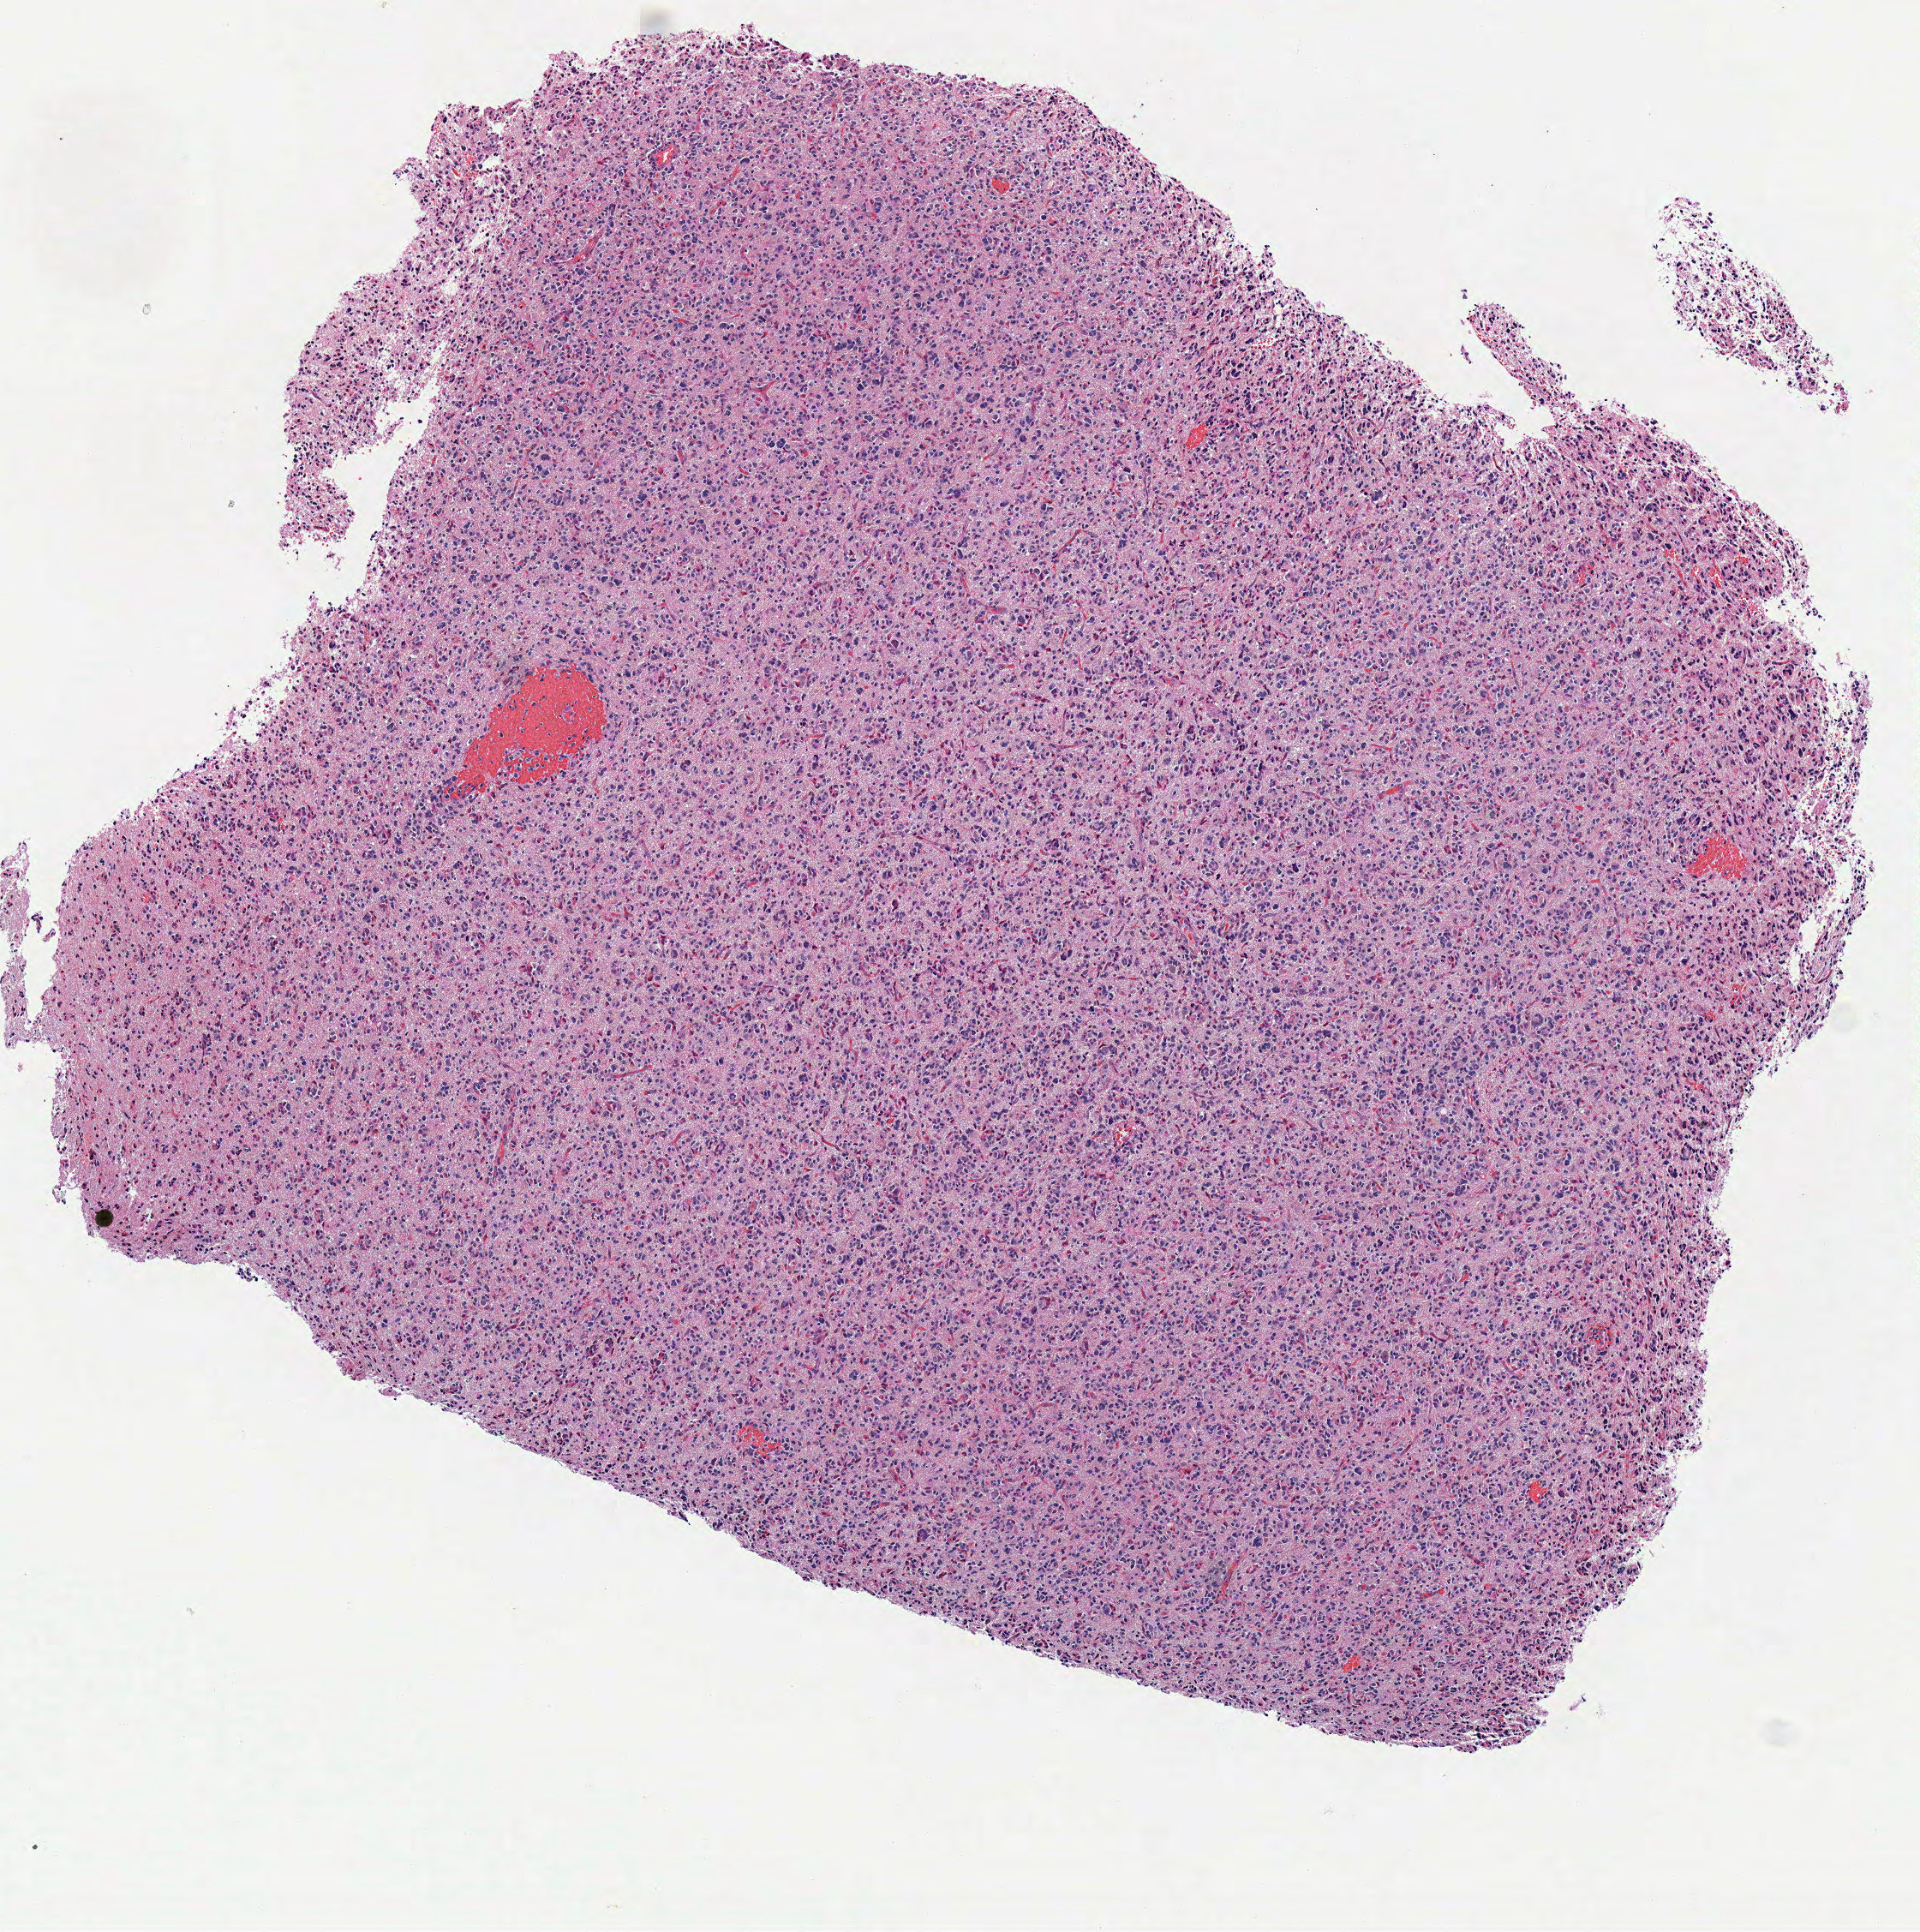
H&E-stained whole-slide image — whole scanned area (about 4.4 x 4.4 mm, acquisition: 40x scan) shown as a low-resolution overview; frozen section; brain, primary tumour sample. Male, age 76 years at initial diagnosis. Pathologist review of this section (percent, as recorded): tumour cells 100%, tumour nuclei 85%, normal cells 0%, stromal cells 0%, necrosis 0%.
Diagnosis: Glioblastoma.